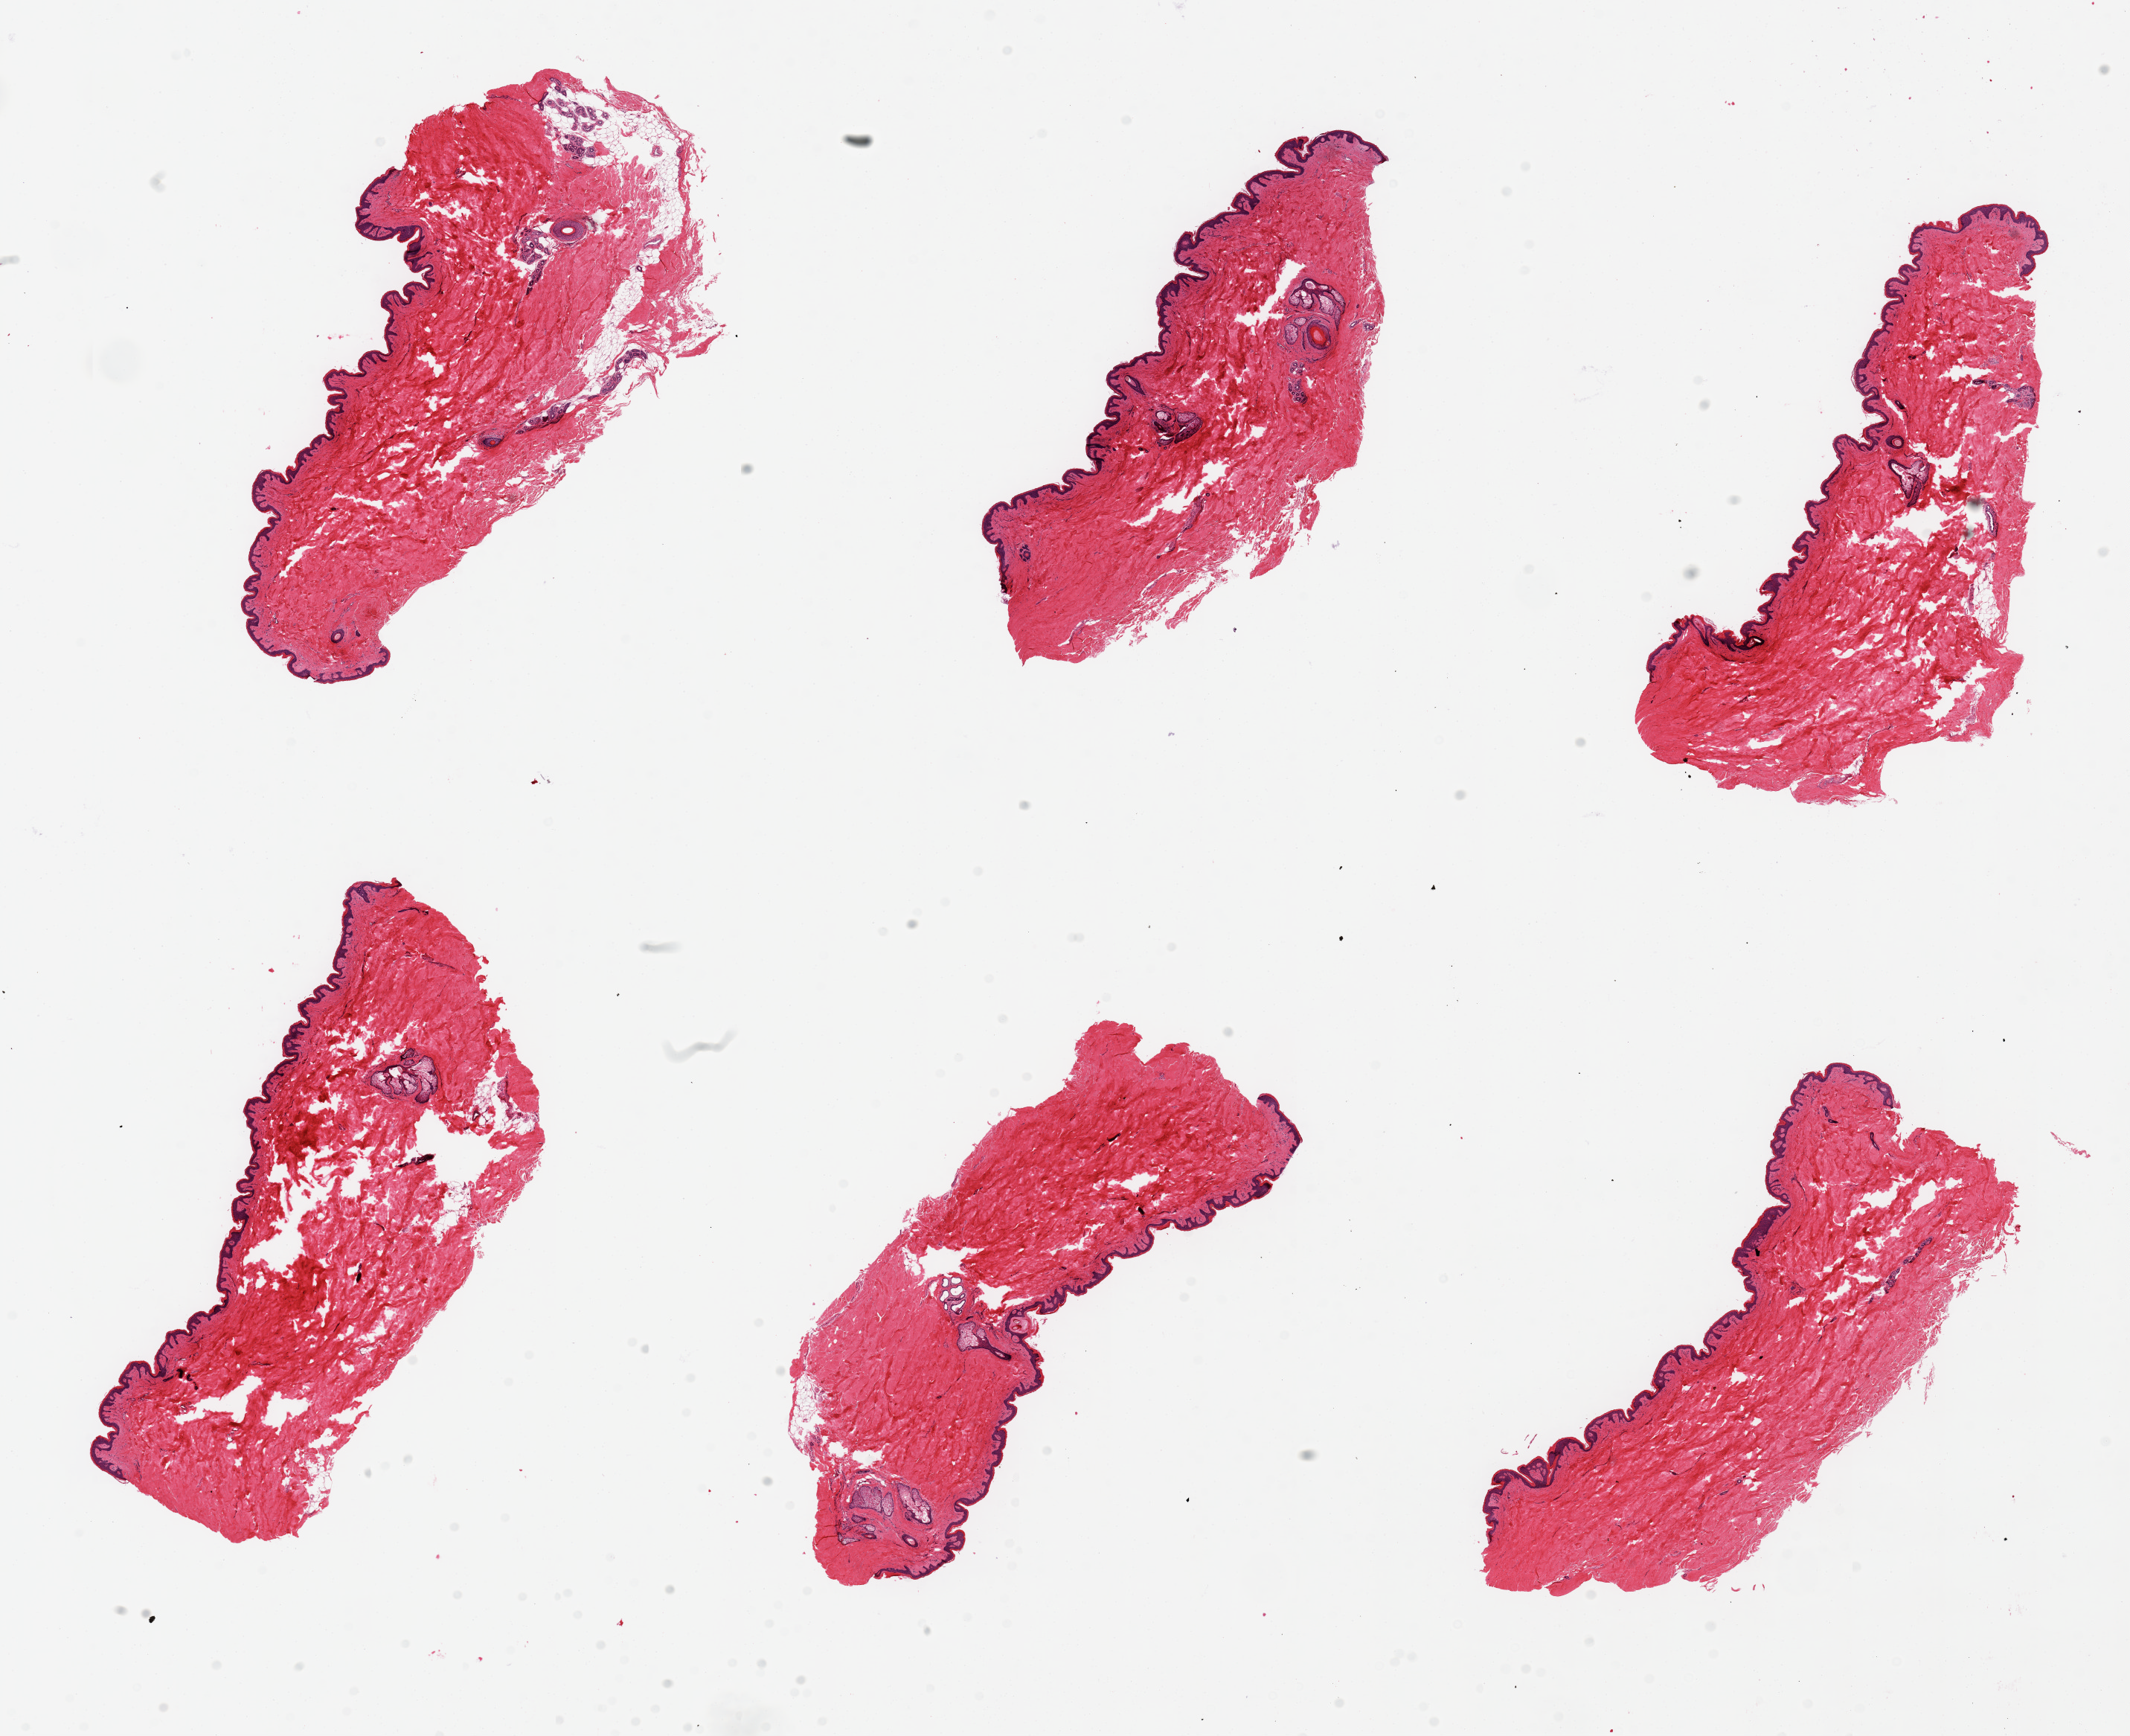
Digitized haematoxylin and eosin-stained section, low-resolution overview of the scanned area, about 22.6 x 18.5 mm (acquisition: 20x scan); PAXgene-fixed, paraffin-embedded tissue; target tissue: skin of suprapubic region; tissue donor sample. Donor sex: male.
Review note (as recorded): 6 pieces, up to 7x4mm; Well trimmed, no subcutaneous adipose.